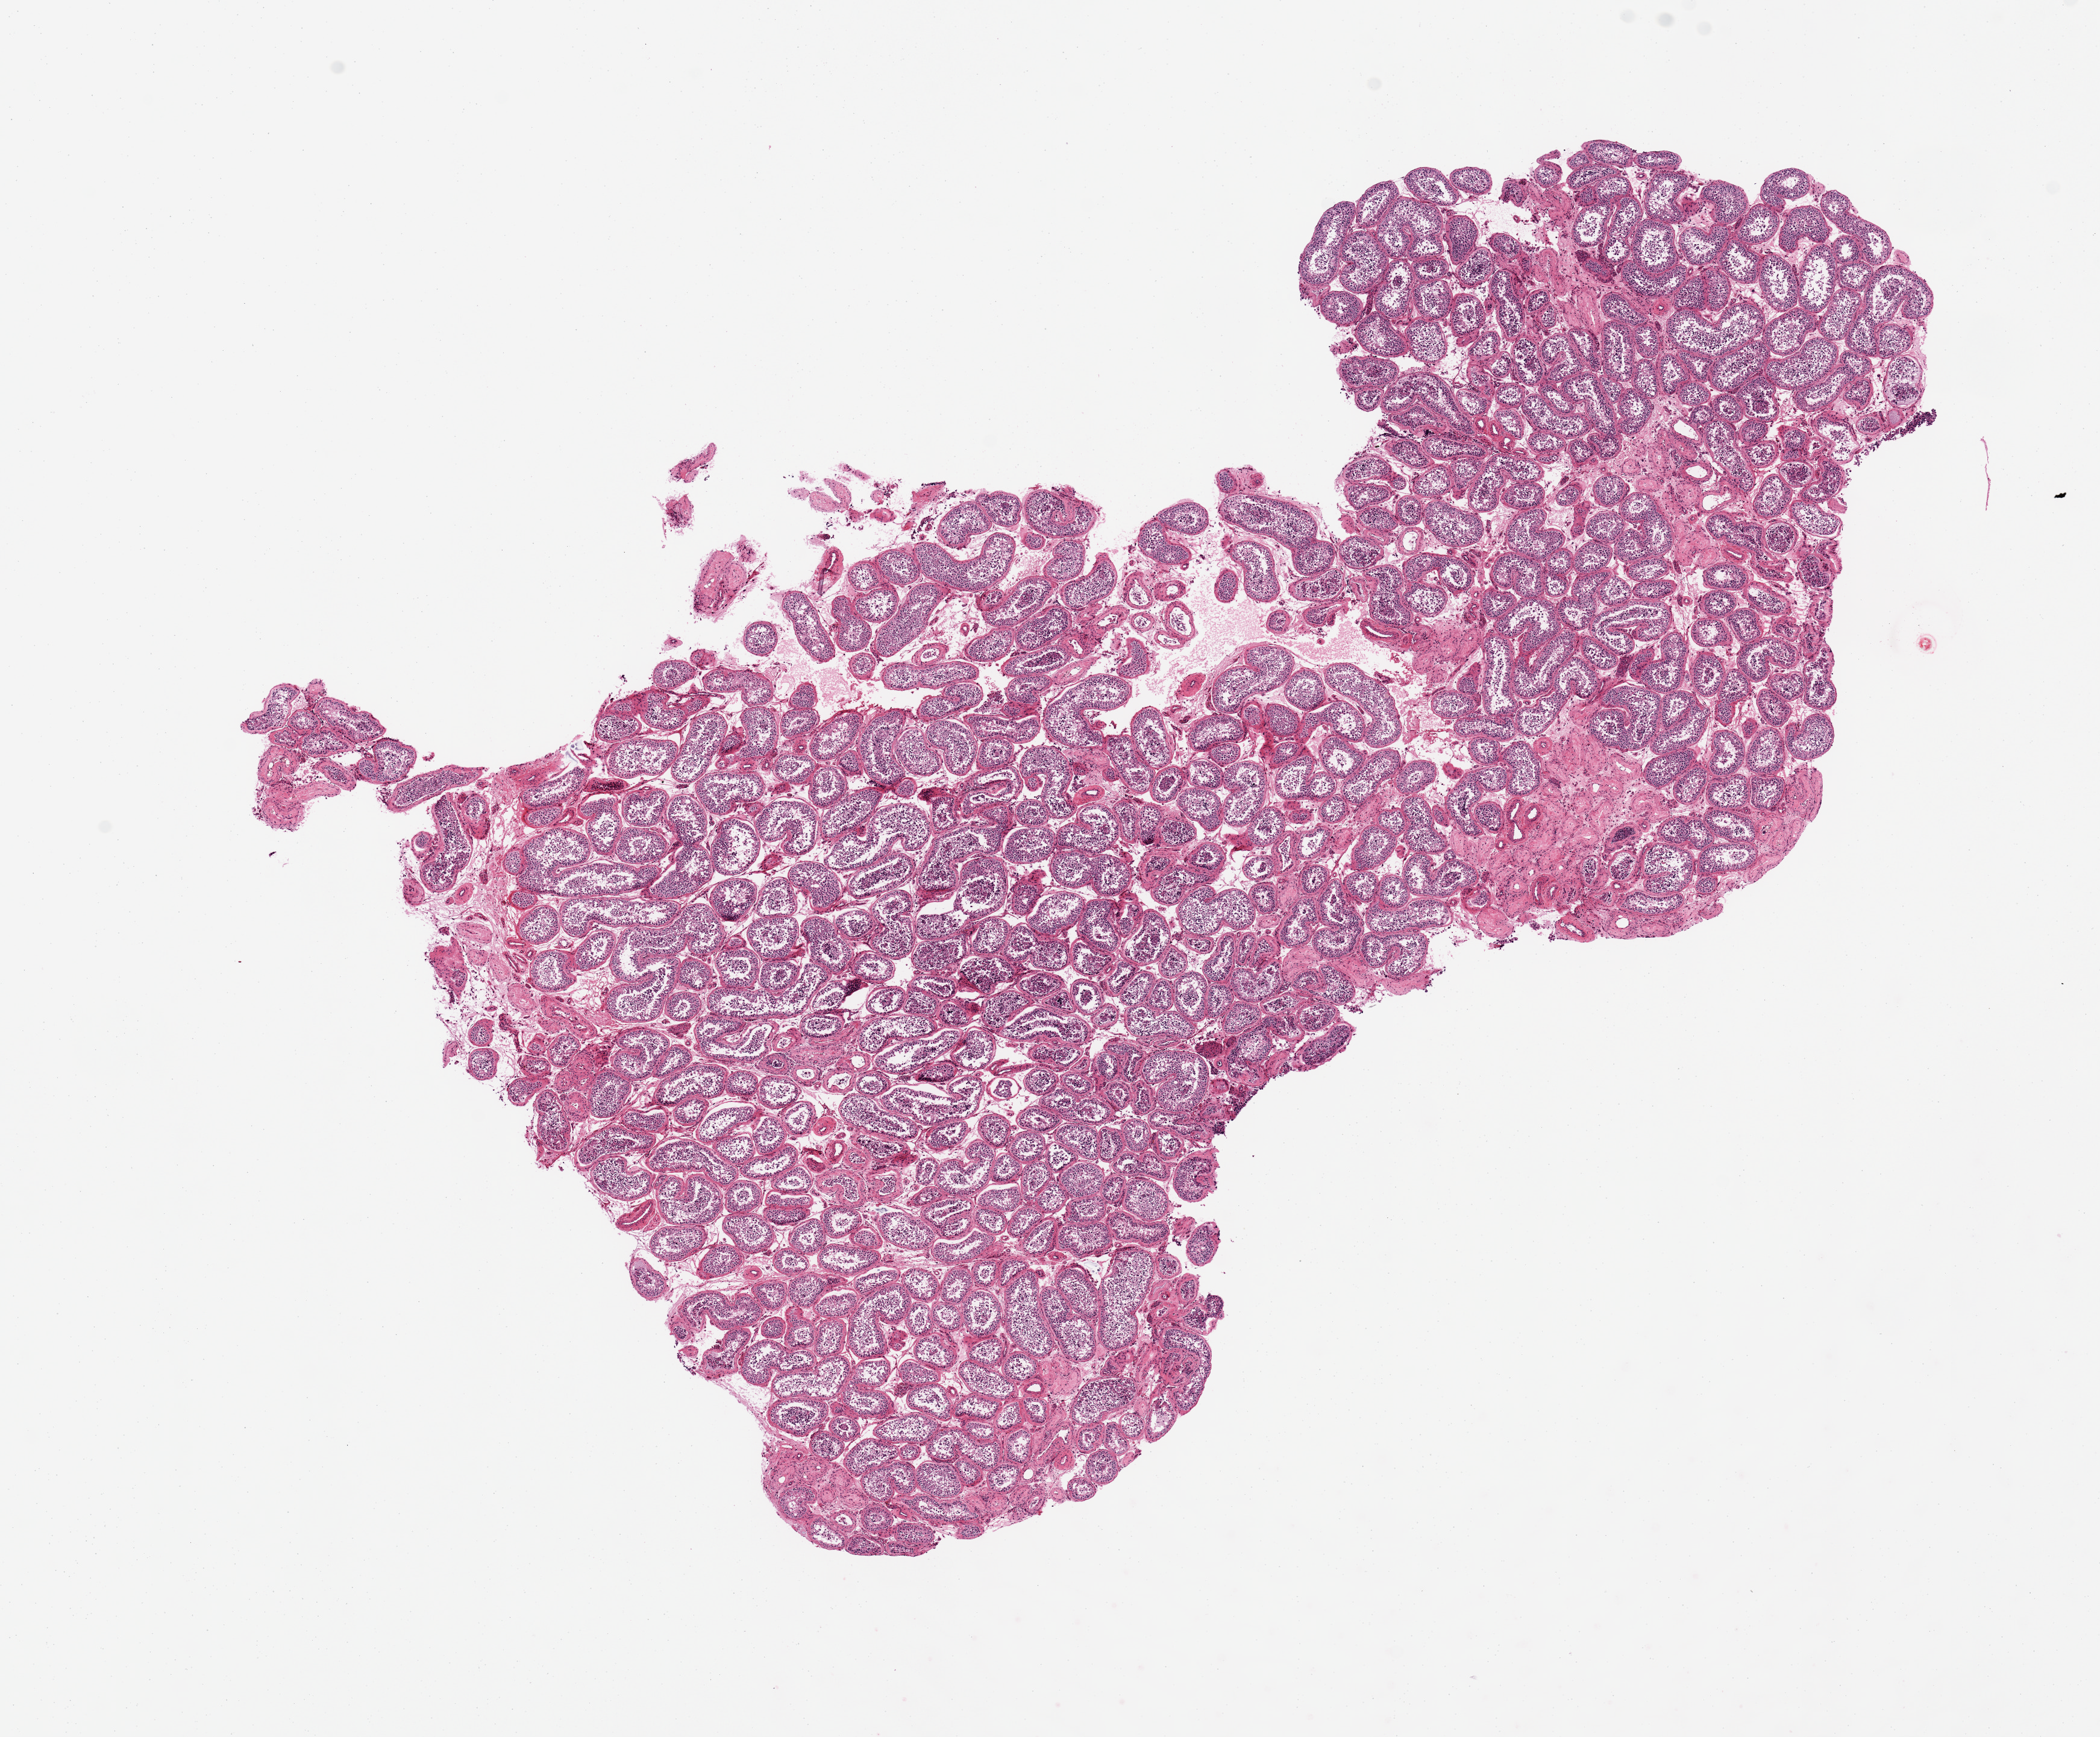
Digitized haematoxylin and eosin-stained section — a low-resolution overview of the entire scanned area, about 13.8 x 11.4 mm (from a 20x scan); PAXgene-fixed paraffin-embedded (PFPE) section; target tissue: testis; donor tissue sample. Donor: male.
- reviewer comment on this tissue sample: 10.5 x 4.5. Complete spermatogenesis is present